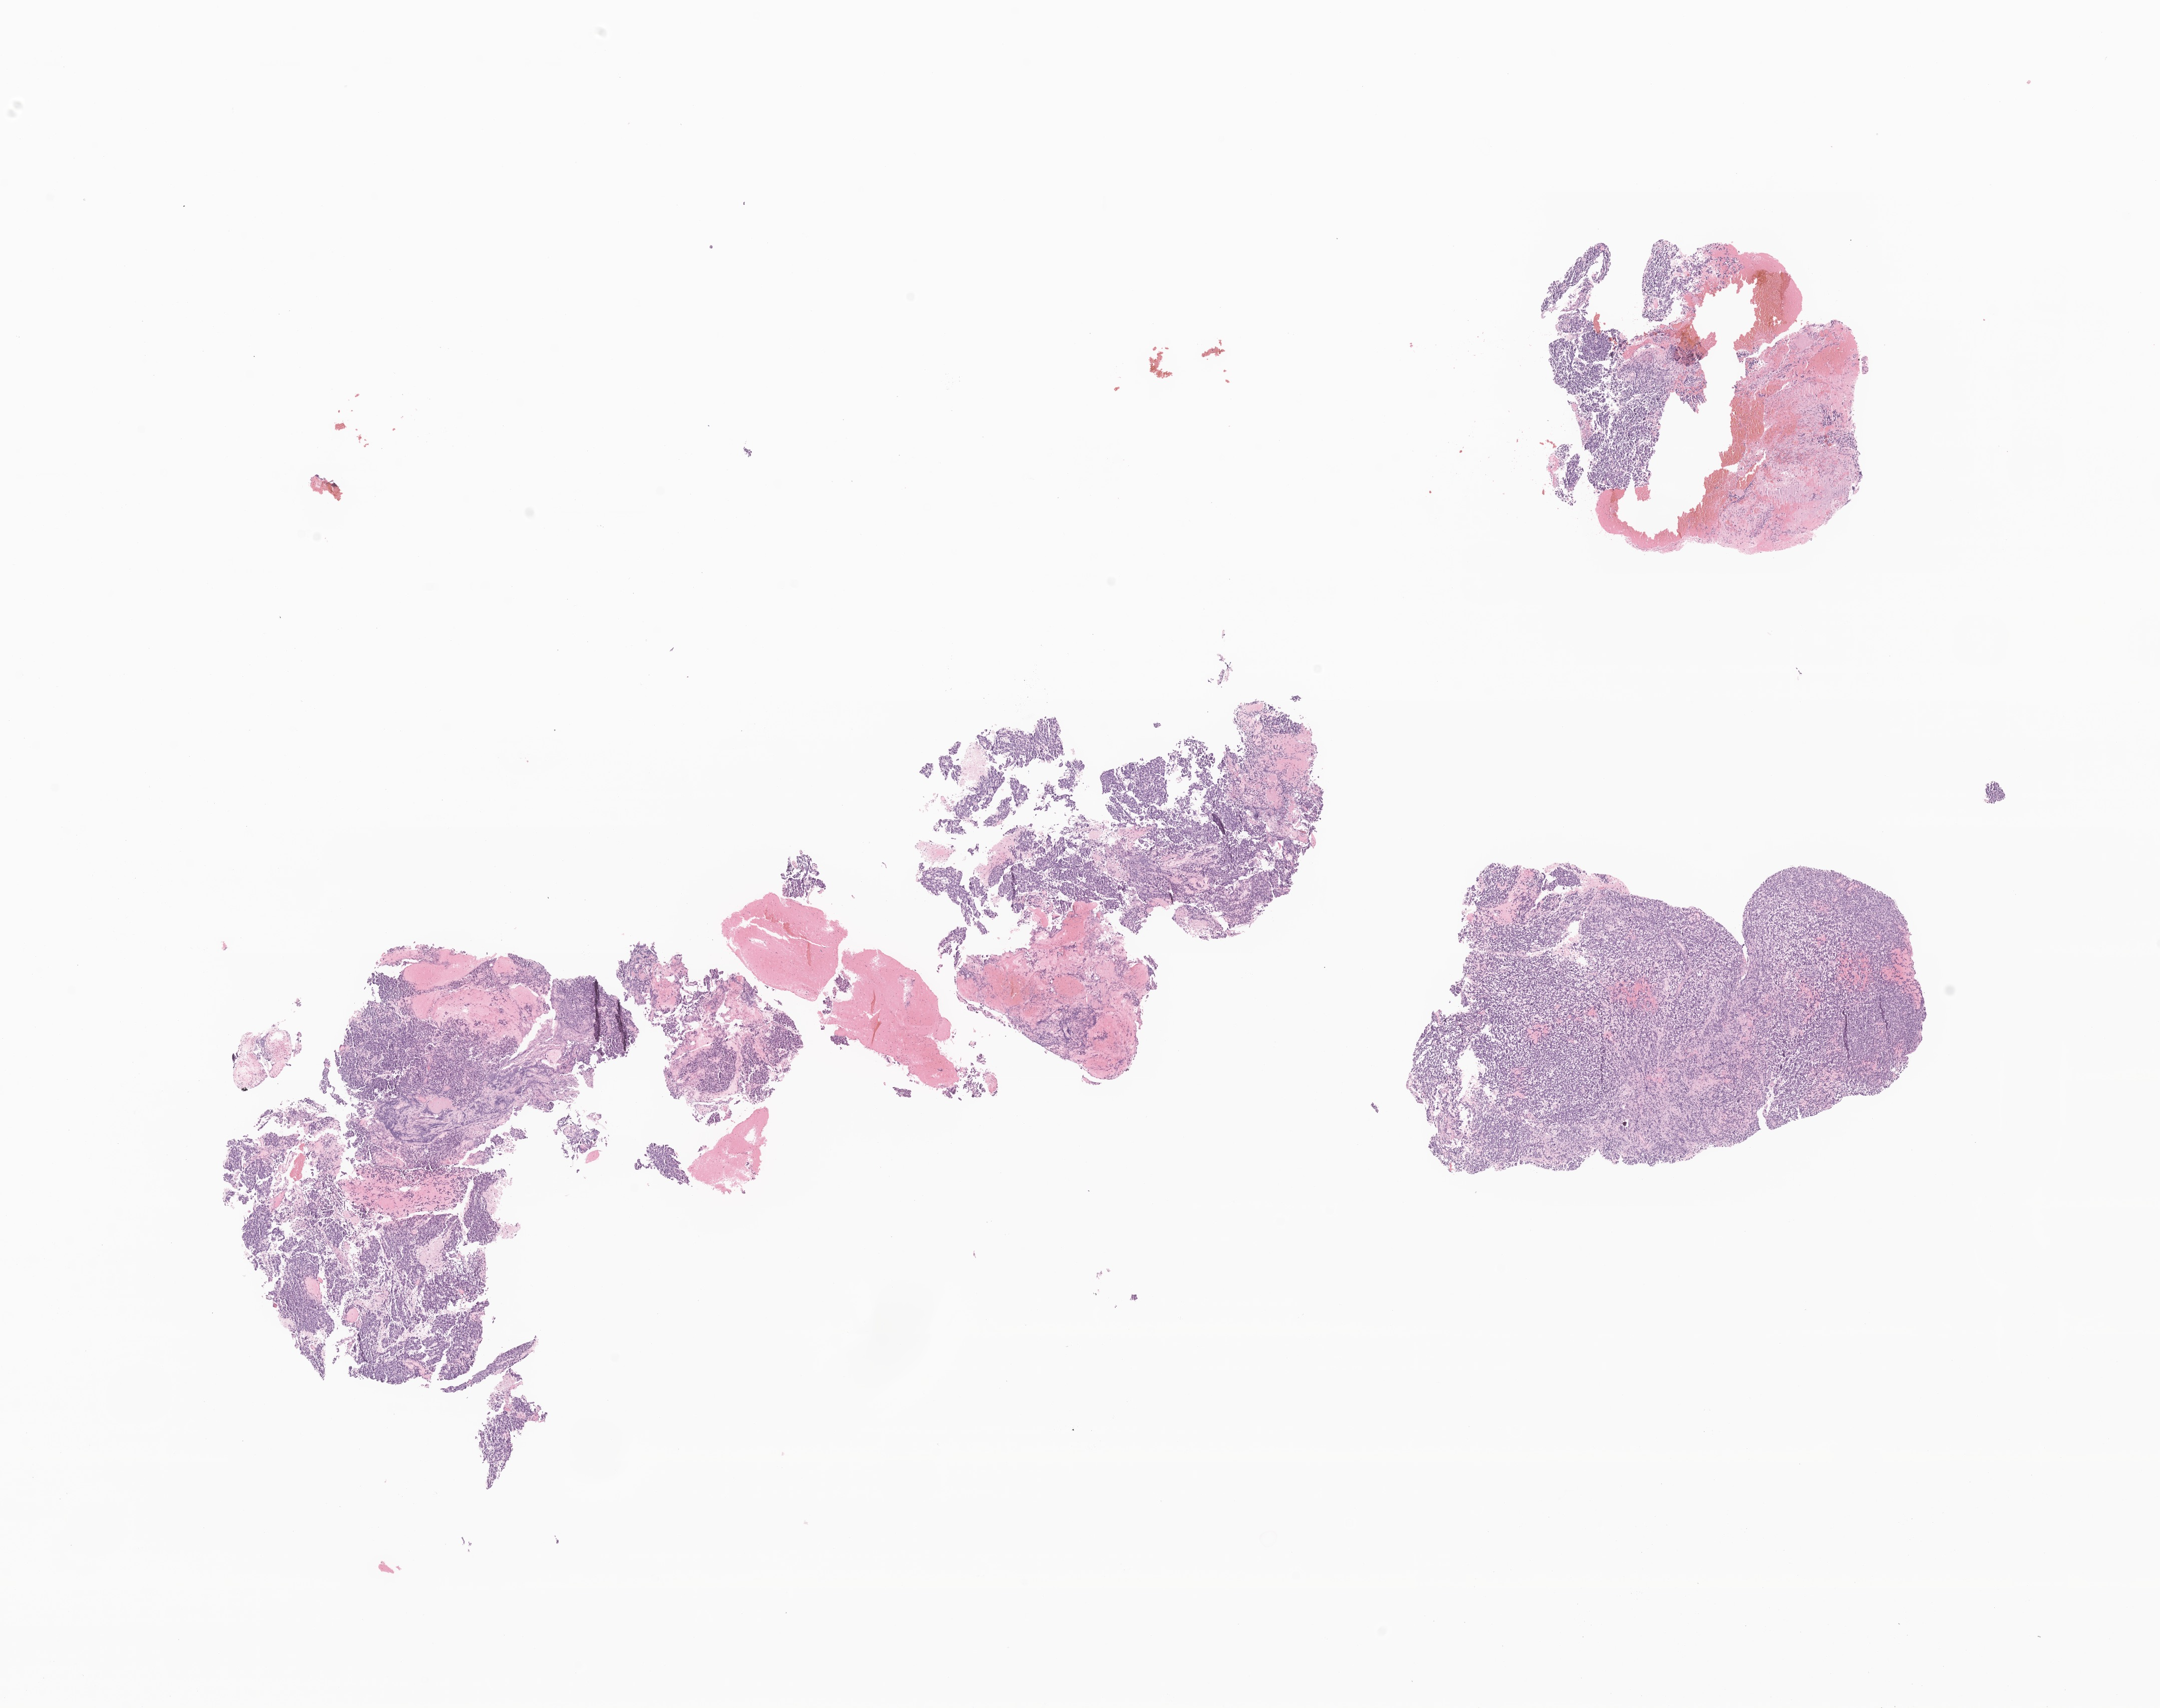
Hematoxylin and eosin (H&E) whole-slide image of tumor tissue from the pineal gland, shown as a low-resolution overview of the whole scanned area (about 18.2 x 14.4 mm), formalin-fixed paraffin-embedded section. Patient: male, age 223 months (18 years 7 months).
Recorded diagnosis: Pineoblastoma.